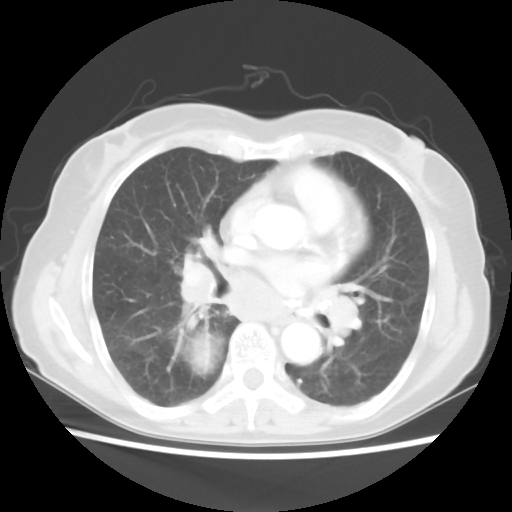
Chest CT, one axial slice; position 30 of 56 along the scan axis; reconstruction kernel STANDARD; 120 kVp; lung window (W 1500 / L -600 HU); 5 mm slice thickness; 512 × 512 image matrix, field of view 332 × 332 mm. Patient: female, 66 years. Case-level facts recorded for this patient, not image findings: clinical TNM (as recorded): T2 N3 M0.
Outlined on this slice (bounding box drawn by a radiologist):
- lung tumour (recorded histology: small cell carcinoma): bounding box (x1, y1, x2, y2) in pixels: (195, 330, 213, 374)